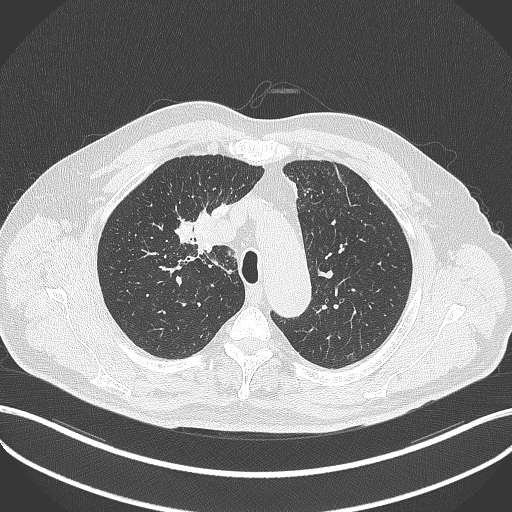
Chest CT, one axial slice. Position 296 of 411 along the scan axis. Reconstruction kernel B70f. Lung window (W 1500 / L -600 HU). 512 × 512 image matrix. Patient: male, 60 years. Case-level facts recorded for this patient, not image findings: clinical TNM (as recorded): T1b N1 M0.
Annotated regions visible in this slice (bounding box drawn by a radiologist):
- lung tumour (recorded histology: squamous cell carcinoma): bounding box <190,207,219,261> (left, top, right, bottom; pixels)